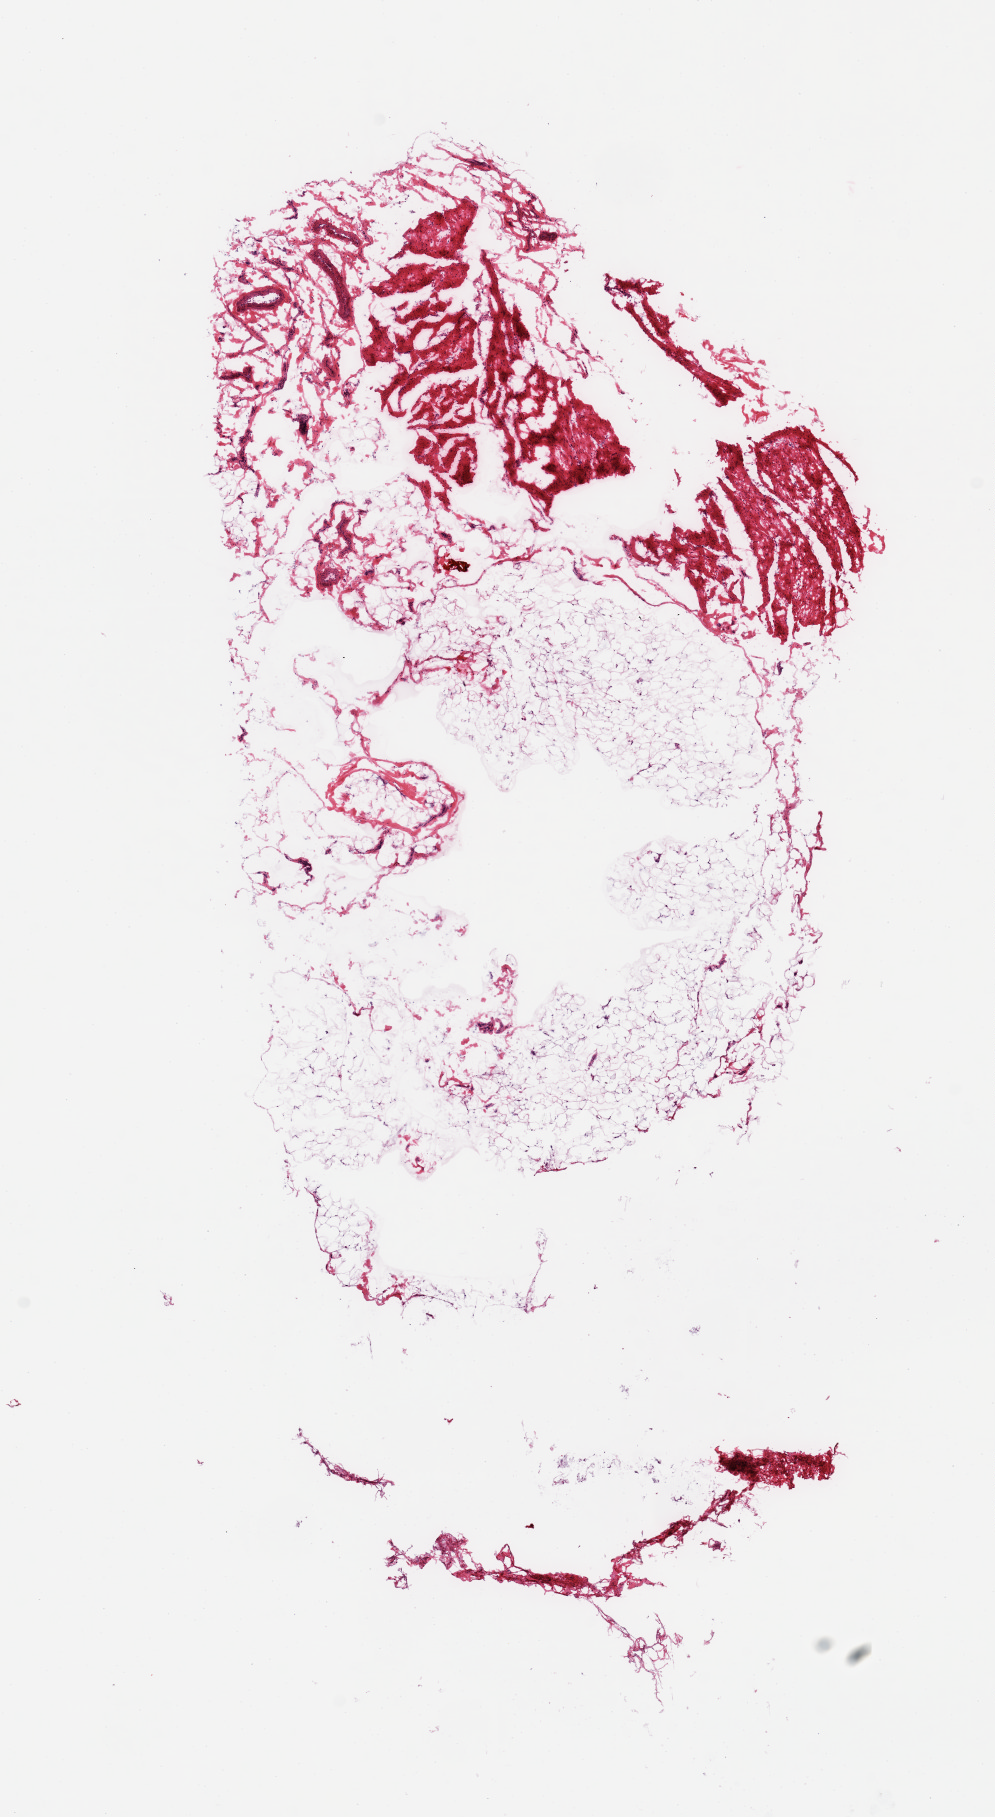
Digitized H&E-stained section, brightfield — a low-resolution overview of the entire scanned area, about 7.9 x 14.4 mm (slide scanned at 20x). Donor: male.
Specimen: frozen section (dry ice); target tissue: esophageal mucous membrane; donor tissue sample.